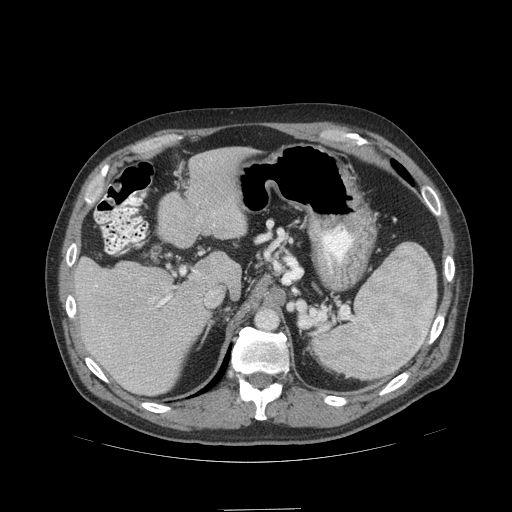
Contrast-enhanced abdominal CT (liver protocol), one axial slice; slice 69 of 99 in the series (ordered by position); 140 kVp; soft-tissue window (W 400 / L 40 HU); 512 × 512 image matrix, field of view 440 × 440 mm. From the clinical record (not read from this slice): diagnosis: hepatocellular carcinoma (patient treated with transarterial chemoembolisation; whether this scan precedes or follows treatment is not stated here); TNM stage (as recorded): Stage-I; Child-Pugh class: A; tumour differentiation: no biopsy; tumour size: 3.6 cm.
Annotated regions visible in this slice (semi-automatic segmentation, software-assisted and operator-edited):
- liver parenchyma outside the tumour (the mass and vessels are separate outlines, so this box may not span the whole liver): box from (x=74, y=146) to (x=251, y=394) px
- liver vessels: (x=94, y=271)–(x=213, y=369)